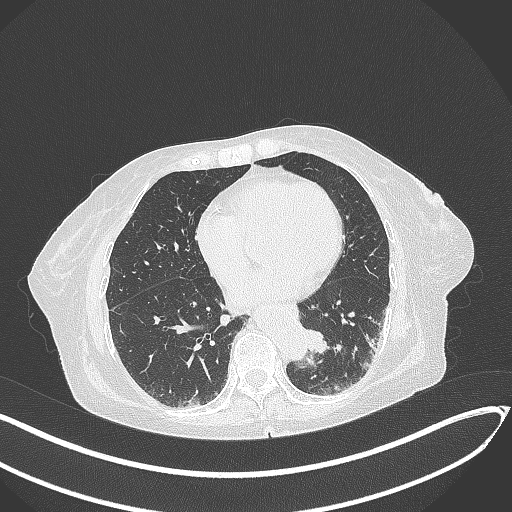
Chest CT, one axial slice; slice 82 of 324 in the series (ordered by position); reconstruction kernel B70f; lung window (W 1500 / L -600 HU); 1 mm slice thickness; 512 × 512 image matrix, field of view 400 × 400 mm. Female patient, age 82 years. Case-level facts recorded for this patient, not image findings: clinical TNM (as recorded): T1b N0 M1.
Structures marked on this image (bounding box drawn by a radiologist):
- lung tumour (recorded histology: adenocarcinoma): bounding box <300,325,338,364> (left, top, right, bottom; pixels)